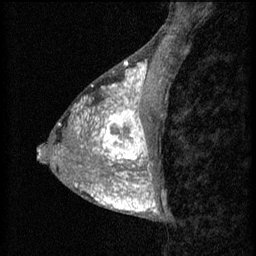
Breast MRI (dynamic contrast-enhanced), one sagittal slice. Slice 23 of 60 in the series (ordered by position). 3 images stored at this slice position (order not interpretable as contrast timing). 1.5 T. TE 4.2 ms, TR 8.2 ms. 256 × 256 image matrix, field of view 180 × 180 mm. Female patient, age 38 years.
Annotated regions visible in this slice (semi-automatic segmentation, software-assisted and operator-edited):
- analysis volume of interest (the breast-tissue region the enhancement analysis was run in; not a lesion): box from (x=95, y=106) to (x=157, y=171) px
- tumour enhancement mask (voxels above the 70 % enhancement threshold inside the analysis volume of interest): (x=95, y=106)–(x=152, y=171)